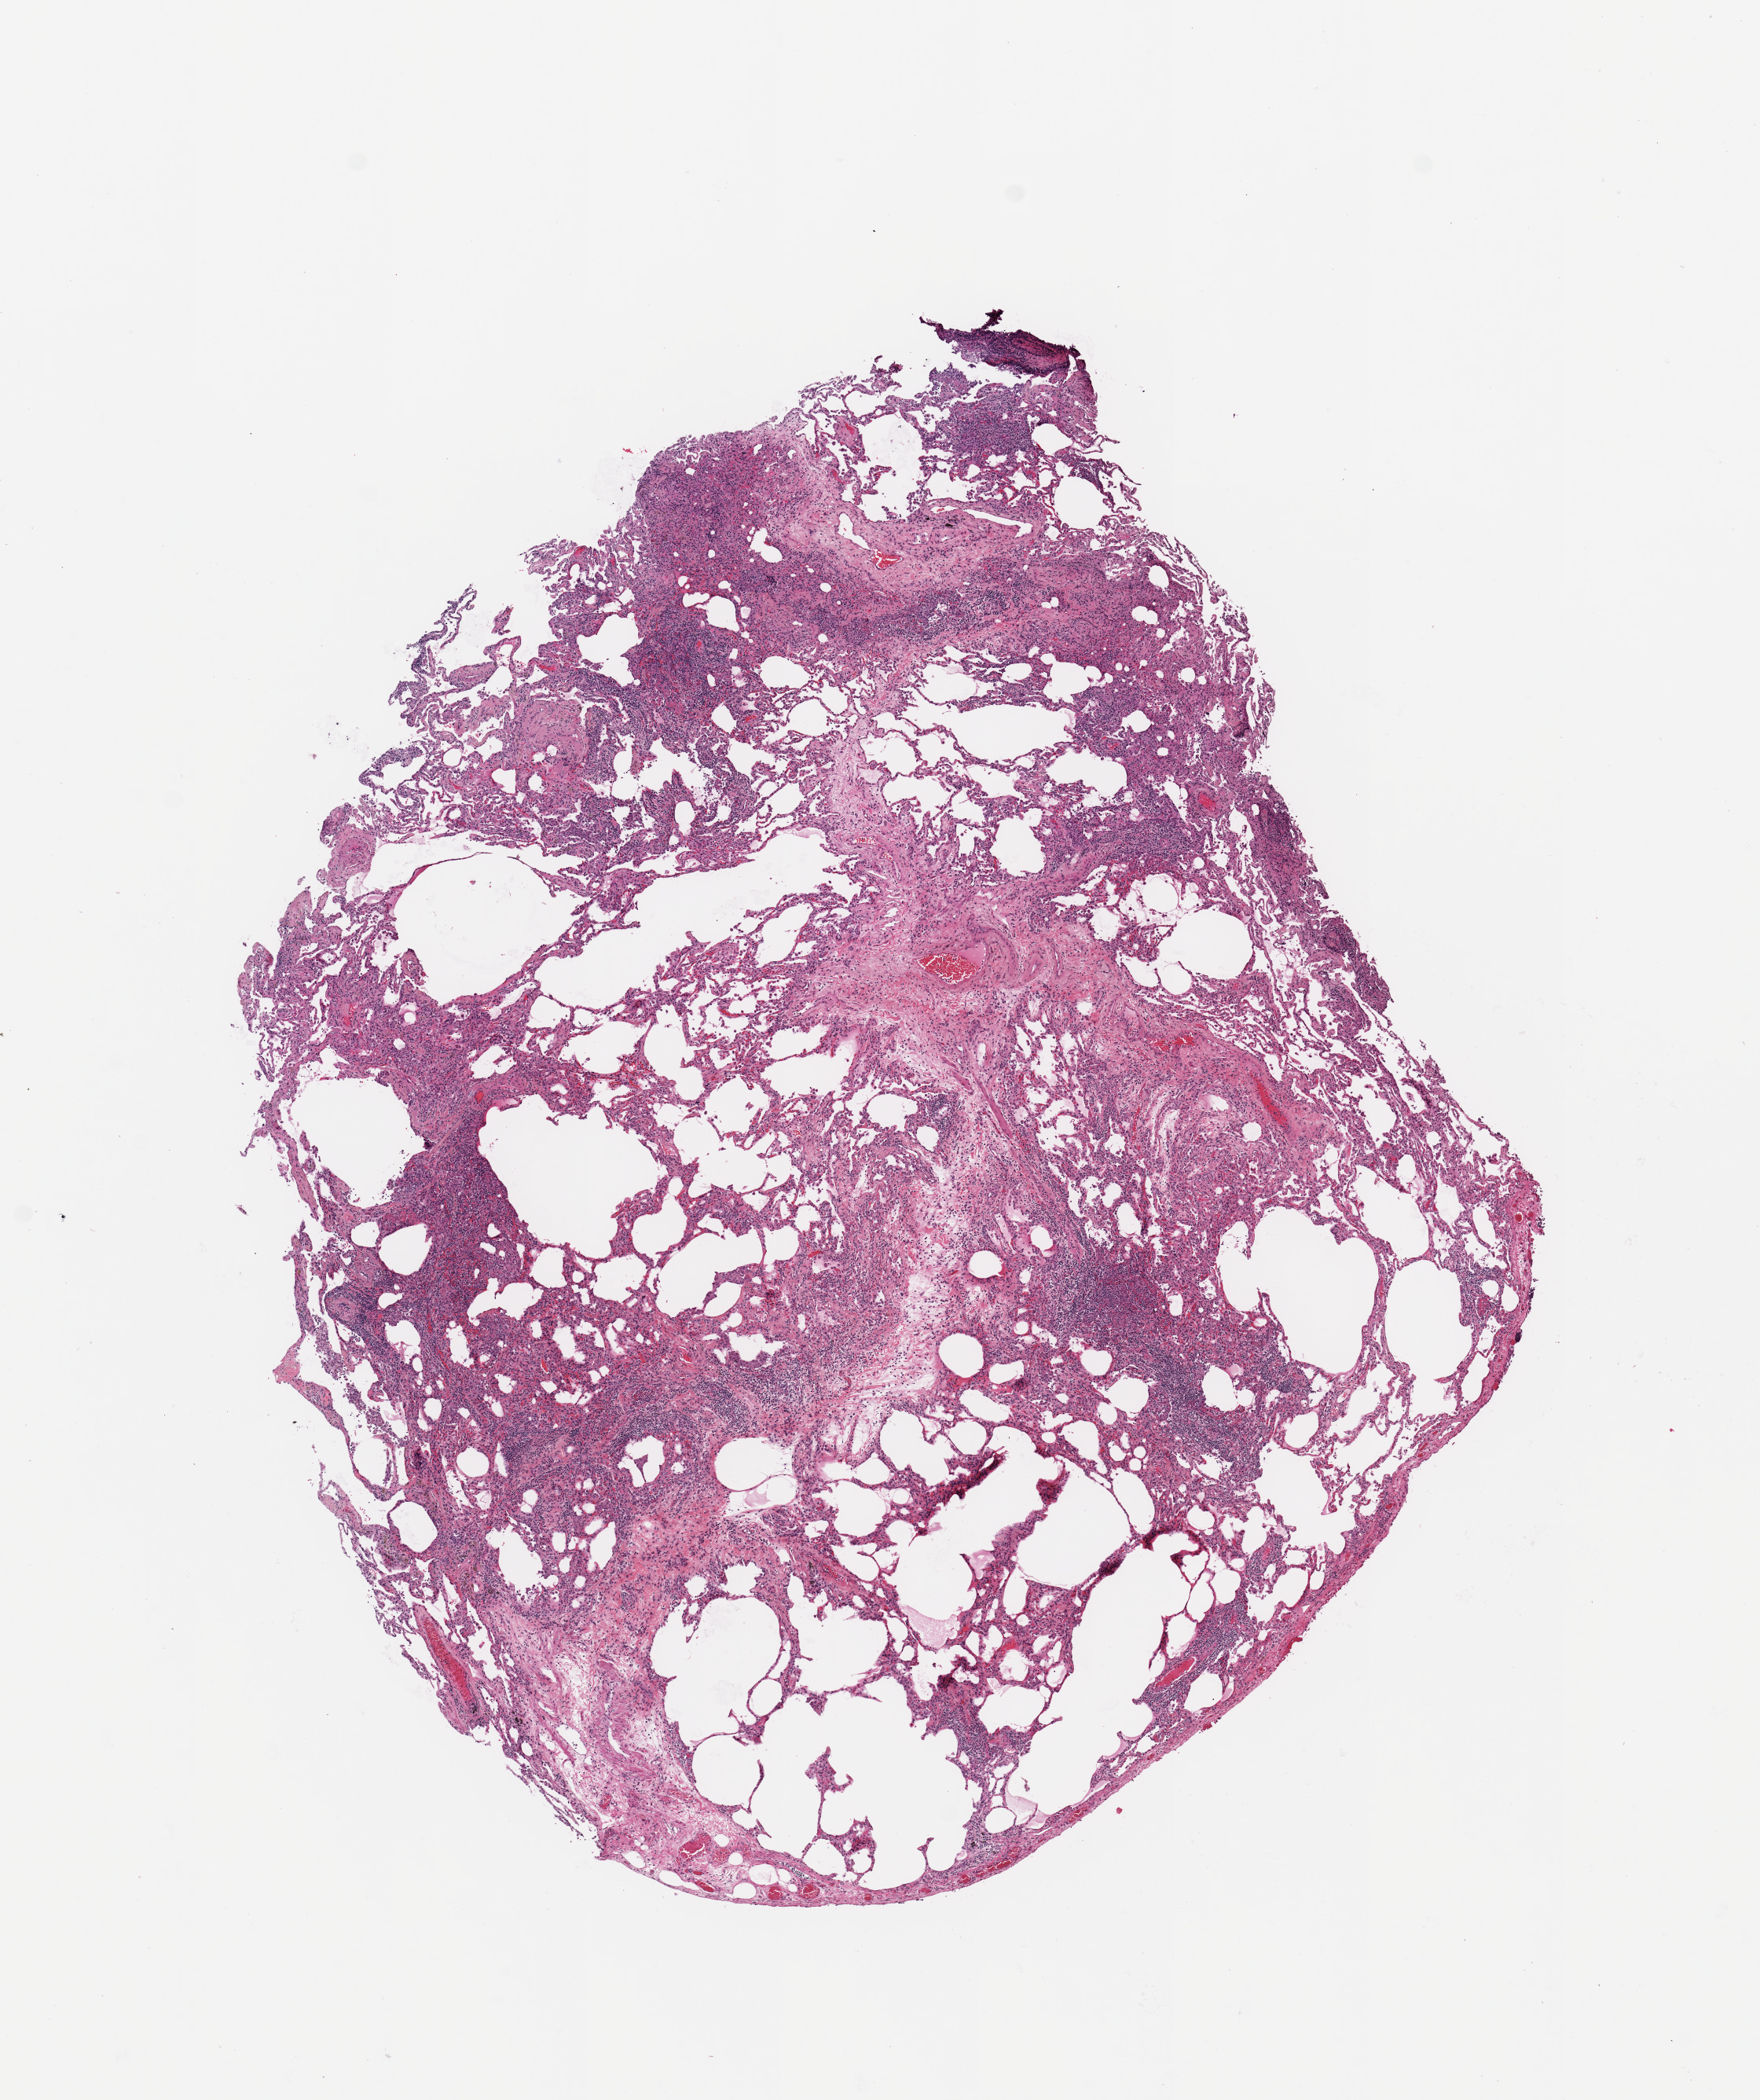
Digitized H&E-stained tissue section (whole slide), a low-resolution overview of the entire scanned area, about 8.9 x 10.6 mm (acquisition: 20x scan), lung, normal (non-tumour) tissue. Patient: male, age 63 years.
This section: normal (non-tumour) tissue from the same patient. Patient diagnosis: Squamous cell carcinoma, NOS.